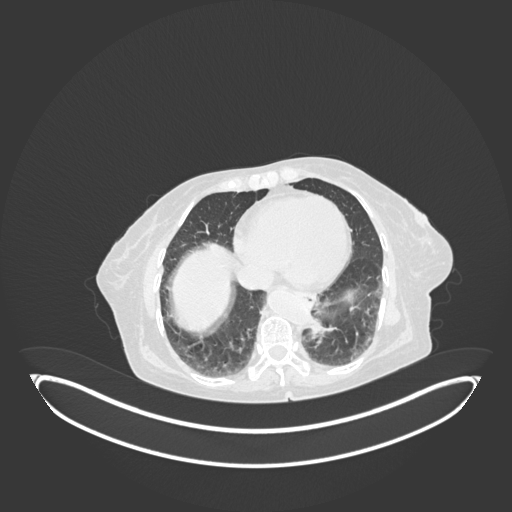
Chest CT, one axial slice; slice 19 of 189 in the series (ordered by position); 120 kVp; lung window (W 1500 / L -600 HU); 512 × 512 image matrix, field of view 500 × 500 mm. Female patient, age 82 years. Case-level facts recorded for this patient, not image findings: clinical TNM (as recorded): T1b N0 M1.
Structures marked on this image (rectangle marked by the reading radiologist):
- lung tumour (recorded histology: adenocarcinoma): box from (x=308, y=312) to (x=340, y=347) px